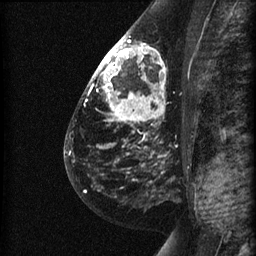
Breast MRI (dynamic contrast-enhanced), one sagittal slice. Slice 35 of 60 in the series (ordered by position). Dynamic contrast-enhanced series, image 2 of 3 at this slice position (ordered by acquisition). 1.5 T. TE 4.2 ms, TR 22.7 ms. 1.5 mm slice thickness. 256 × 256 image matrix, field of view 180 × 180 mm. Female patient, age 48 years. From the clinical record (not read from this slice): setting: breast cancer imaged before/during neoadjuvant chemotherapy; receptor status: triple-negative.
Structures marked on this image (semi-automatic segmentation, software-assisted and operator-edited):
- analysis volume of interest (the breast-tissue region the enhancement analysis was run in; not a lesion): bounding box <89,27,191,180> (left, top, right, bottom; pixels)
- tumour enhancement mask (voxels above the 90 % enhancement threshold inside the analysis volume of interest): <92,37,163,109>